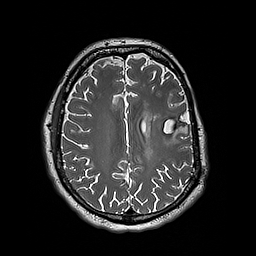
Brain MRI from a brain-tumour surgery series, one axial slice; position 76 of 192 along the scan axis; 1 mm slice thickness; 256 × 256 image matrix. From the clinical record (not read from this slice): histopathology: Astrocytoma; WHO grade: 3.
Annotated regions visible in this slice (expert manual segmentation):
- tumour: bounding box (x1, y1, x2, y2) in pixels: (155, 122, 165, 132)